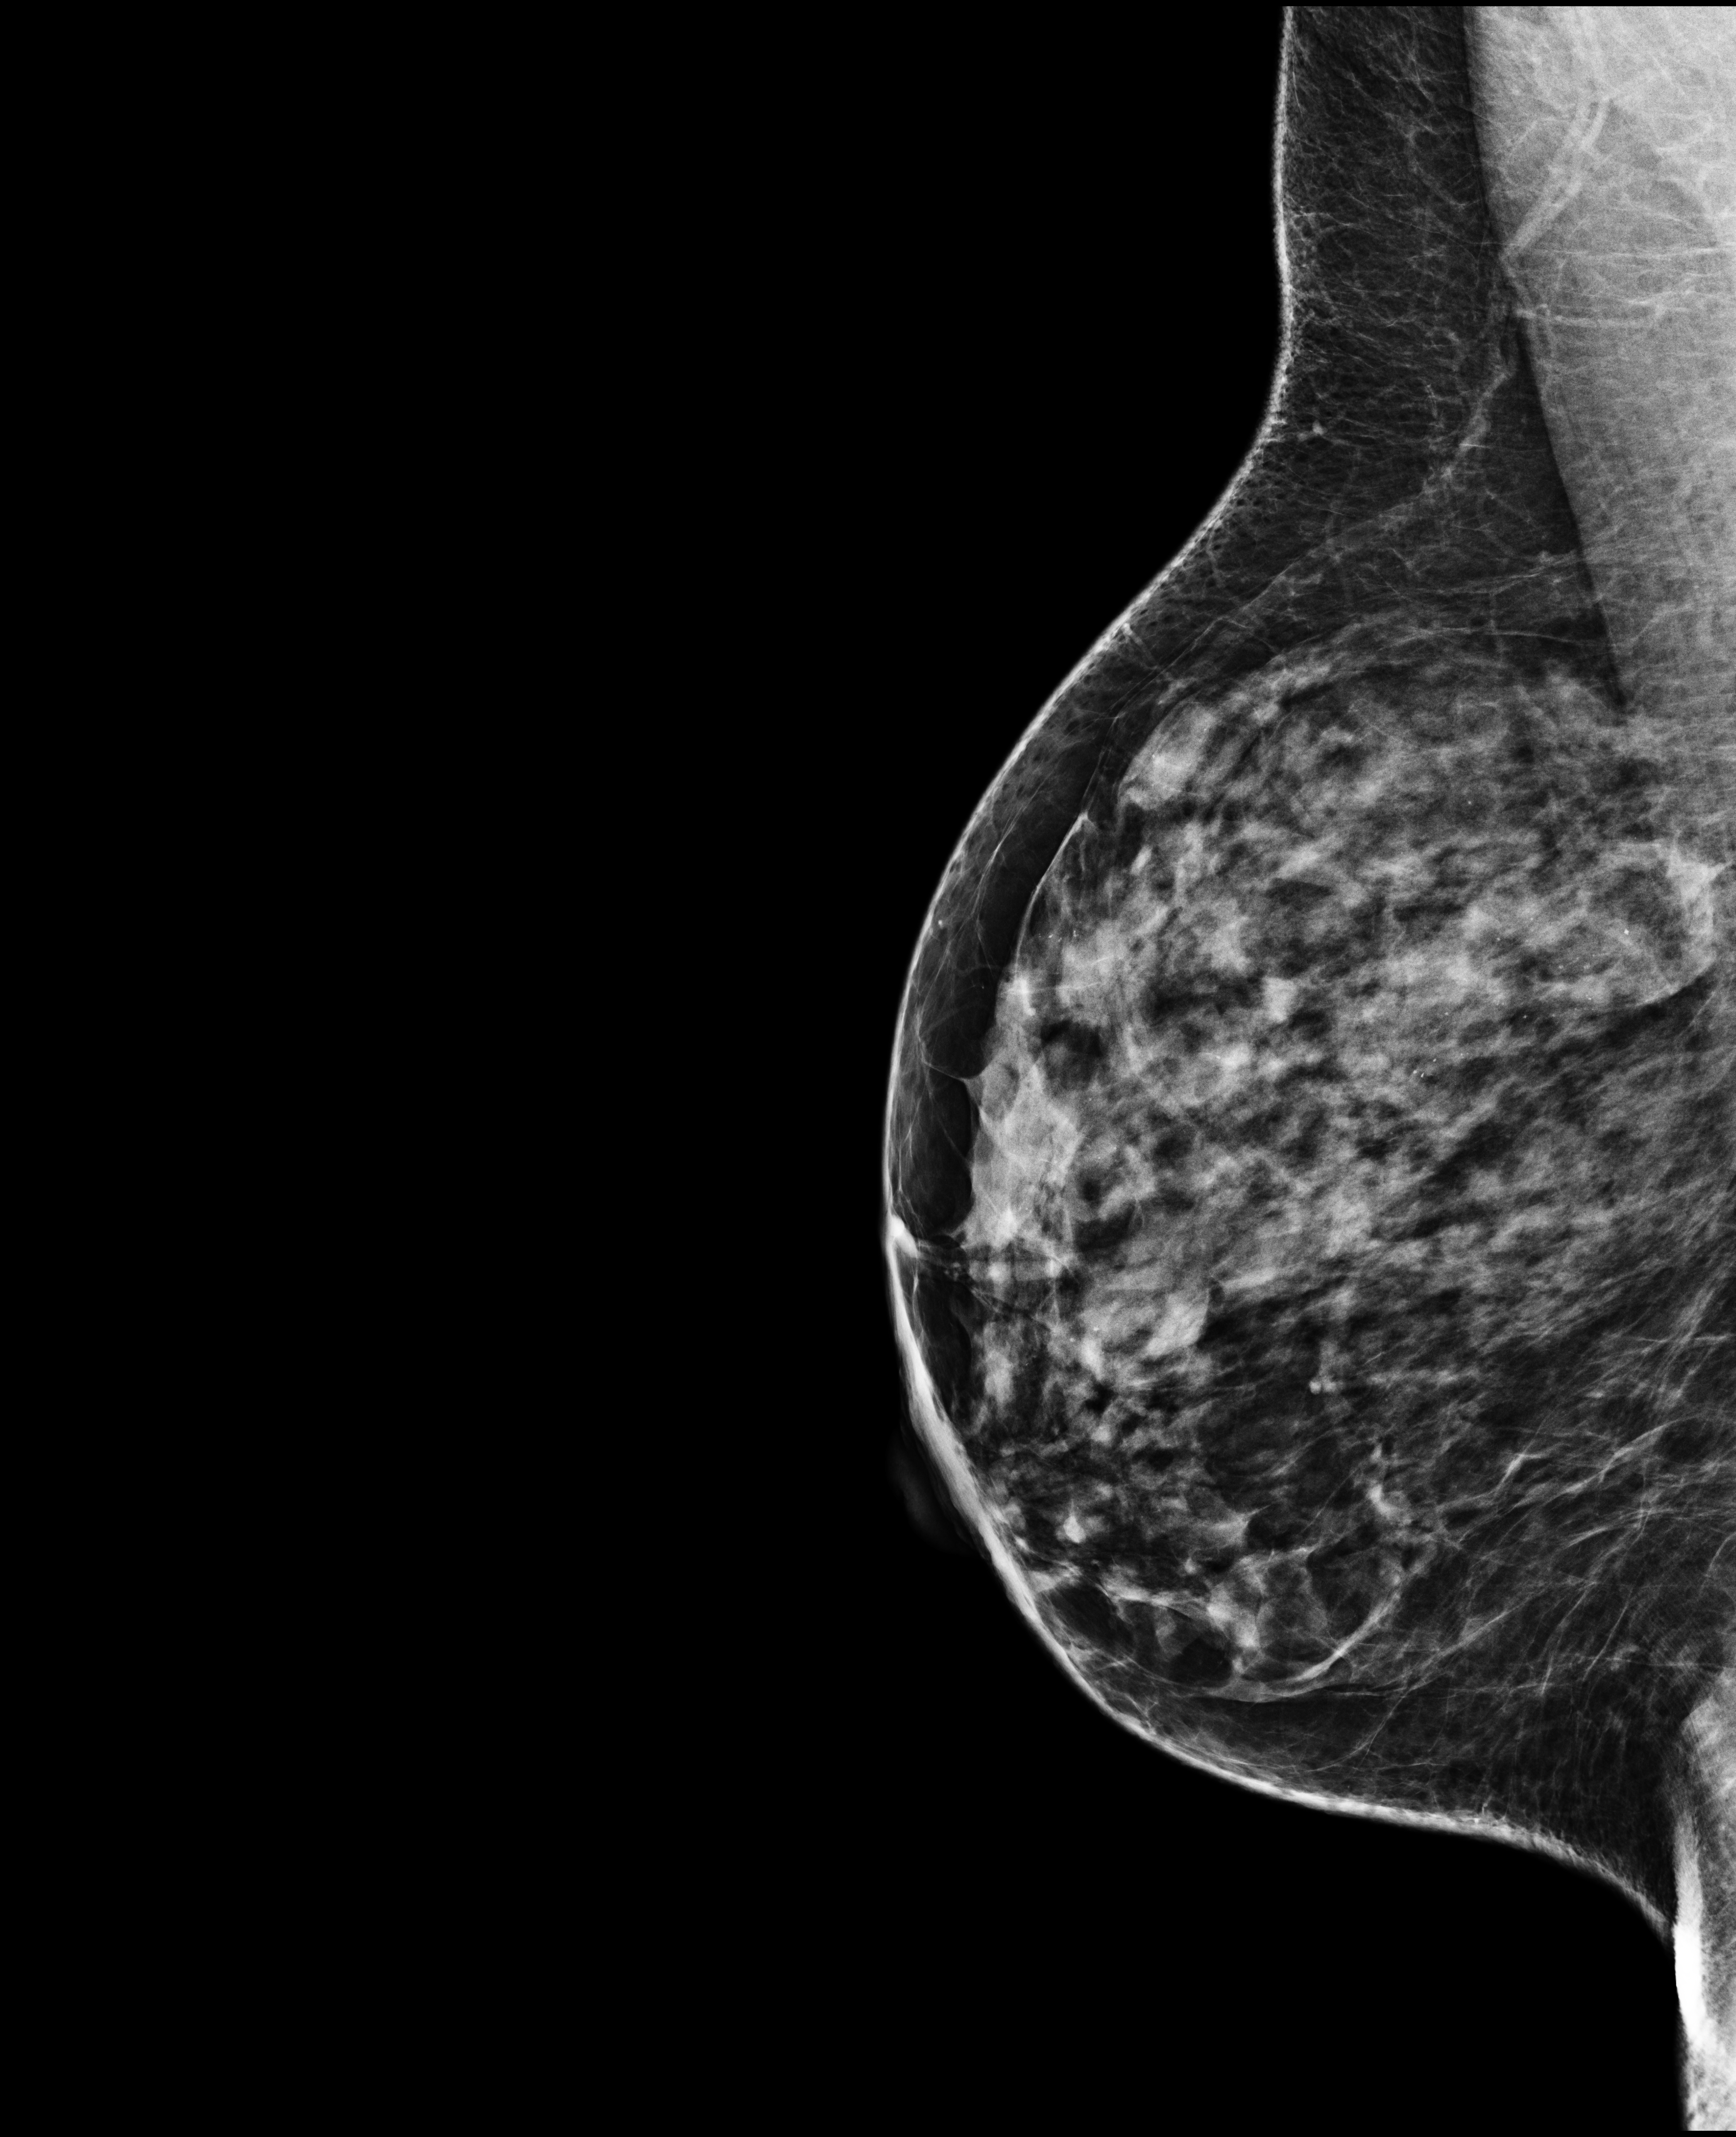
Full-field digital mammogram (FFDM); right breast; MLO view; screening examination; system: Selenia Dimensions. Patient: female, 51 years.
Breast density at the screening exam (both breasts): heterogeneously dense (BI-RADS density category c). Final BI-RADS category for the screening round (tomosynthesis exam, both breasts): category 1. Recall: no recall after this screen.